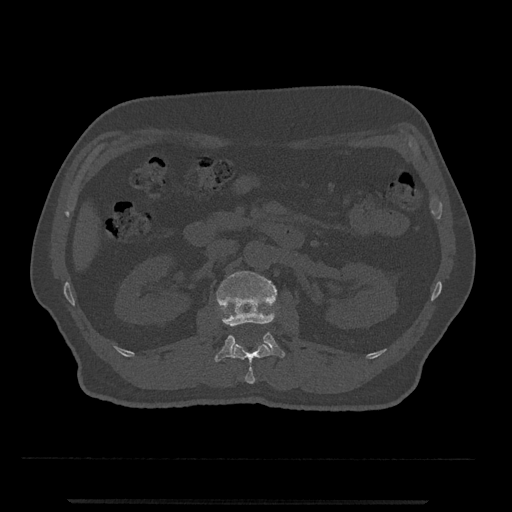
CT including the spine, one axial slice; reconstruction kernel Br40s/3; 120 kVp; bone window (W 1800 / L 400 HU); 0.5 mm slice thickness; 512 × 512 image matrix, field of view 419 × 419 mm. Patient: male, 63 years. From the clinical record (not read from this slice): primary cancer: prostate.
Outlined on this slice (semi-automatically segmented with operator editing):
- L1 vertebra: bounding box [x1, y1, x2, y2] px = [231, 326, 272, 384]
- L2 vertebra: [214, 271, 285, 362]